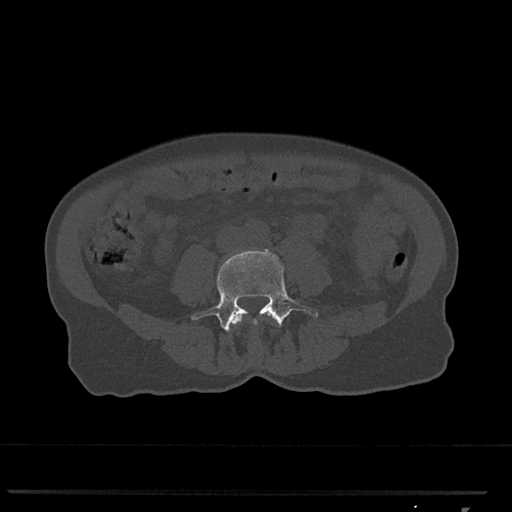
CT including the spine, one axial slice. Slice 224 of 793 in the series (ordered by position). Reconstruction kernel Br40s/3. Bone window (W 1800 / L 400 HU). 0.5 mm slice thickness. 512 × 512 image matrix, field of view 380 × 380 mm. Female patient, age 62 years. From the clinical record (not read from this slice): primary cancer: renal.
Outlined on this slice (semi-automatically segmented with operator editing):
- L3 vertebra: bounding box <230,314,274,349> (left, top, right, bottom; pixels)
- L4 vertebra: <191,250,318,332>